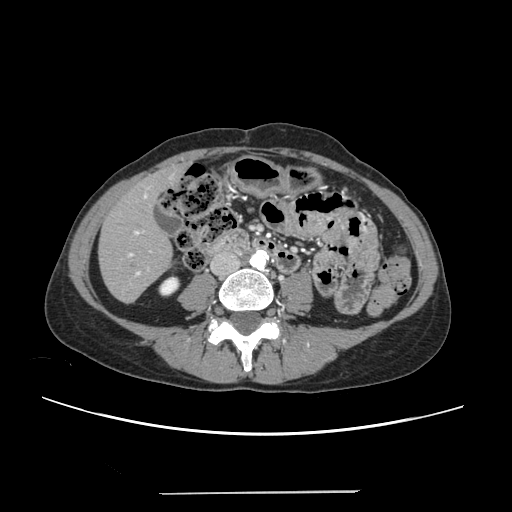
Contrast-enhanced abdominal CT, one axial slice. Slice 60 of 240 in the series (ordered by position). 120 kVp. Intravenous contrast given. Soft-tissue window (W 400 / L 40 HU). 1.25 mm slice thickness. 512 × 512 image matrix, field of view 371 × 371 mm. Female patient, age 60 years. From the clinical record (not read from this slice): diagnosis: colorectal cancer liver metastases, imaged before liver resection; multiple liver metastases: no; largest metastasis: 1.5 cm; disease in both lobes: no.
Outlined on this slice (expert manual segmentation):
- liver: bounding box <100,168,182,302> (left, top, right, bottom; pixels)
- planned liver remnant (the part of the liver to remain after resection): <100,172,172,302>
- portal vein (with intrahepatic branches): <128,192,149,275>